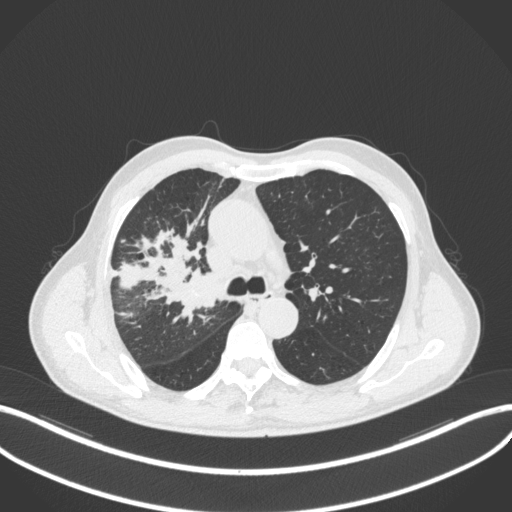
Chest CT, one axial slice; position 326 of 490 along the scan axis; reconstruction kernel B31f; lung window (W 1500 / L -600 HU); 1 mm slice thickness; 512 × 512 image matrix. Male patient, age 69 years. Case-level facts recorded for this patient, not image findings: clinical TNM (as recorded): T2a N0 M0.
Structures marked on this image (bounding box drawn by a radiologist):
- lung tumour (recorded histology: adenocarcinoma): bounding box (x1, y1, x2, y2) in pixels: (177, 269, 220, 313)